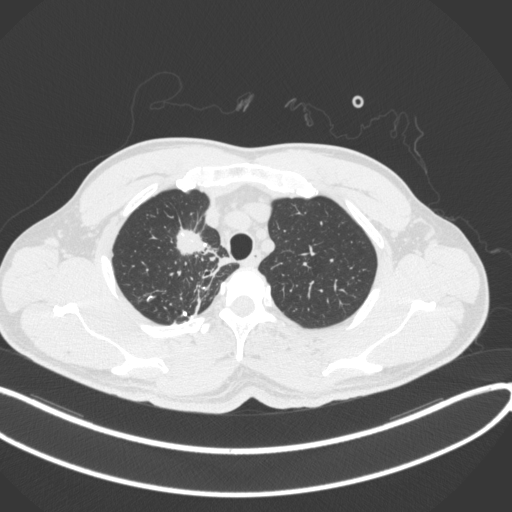
Chest CT, one axial slice. Position 313 of 391 along the scan axis. 120 kVp. Lung window (W 1500 / L -600 HU). 1 mm slice thickness. 512 × 512 image matrix, field of view 400 × 400 mm. Patient: male, 48 years. Case-level facts recorded for this patient, not image findings: clinical TNM (as recorded): T1c N1 M1.
Structures marked on this image (bounding box drawn by a radiologist):
- lung tumour (recorded histology: adenocarcinoma): box from (x=170, y=225) to (x=210, y=259) px